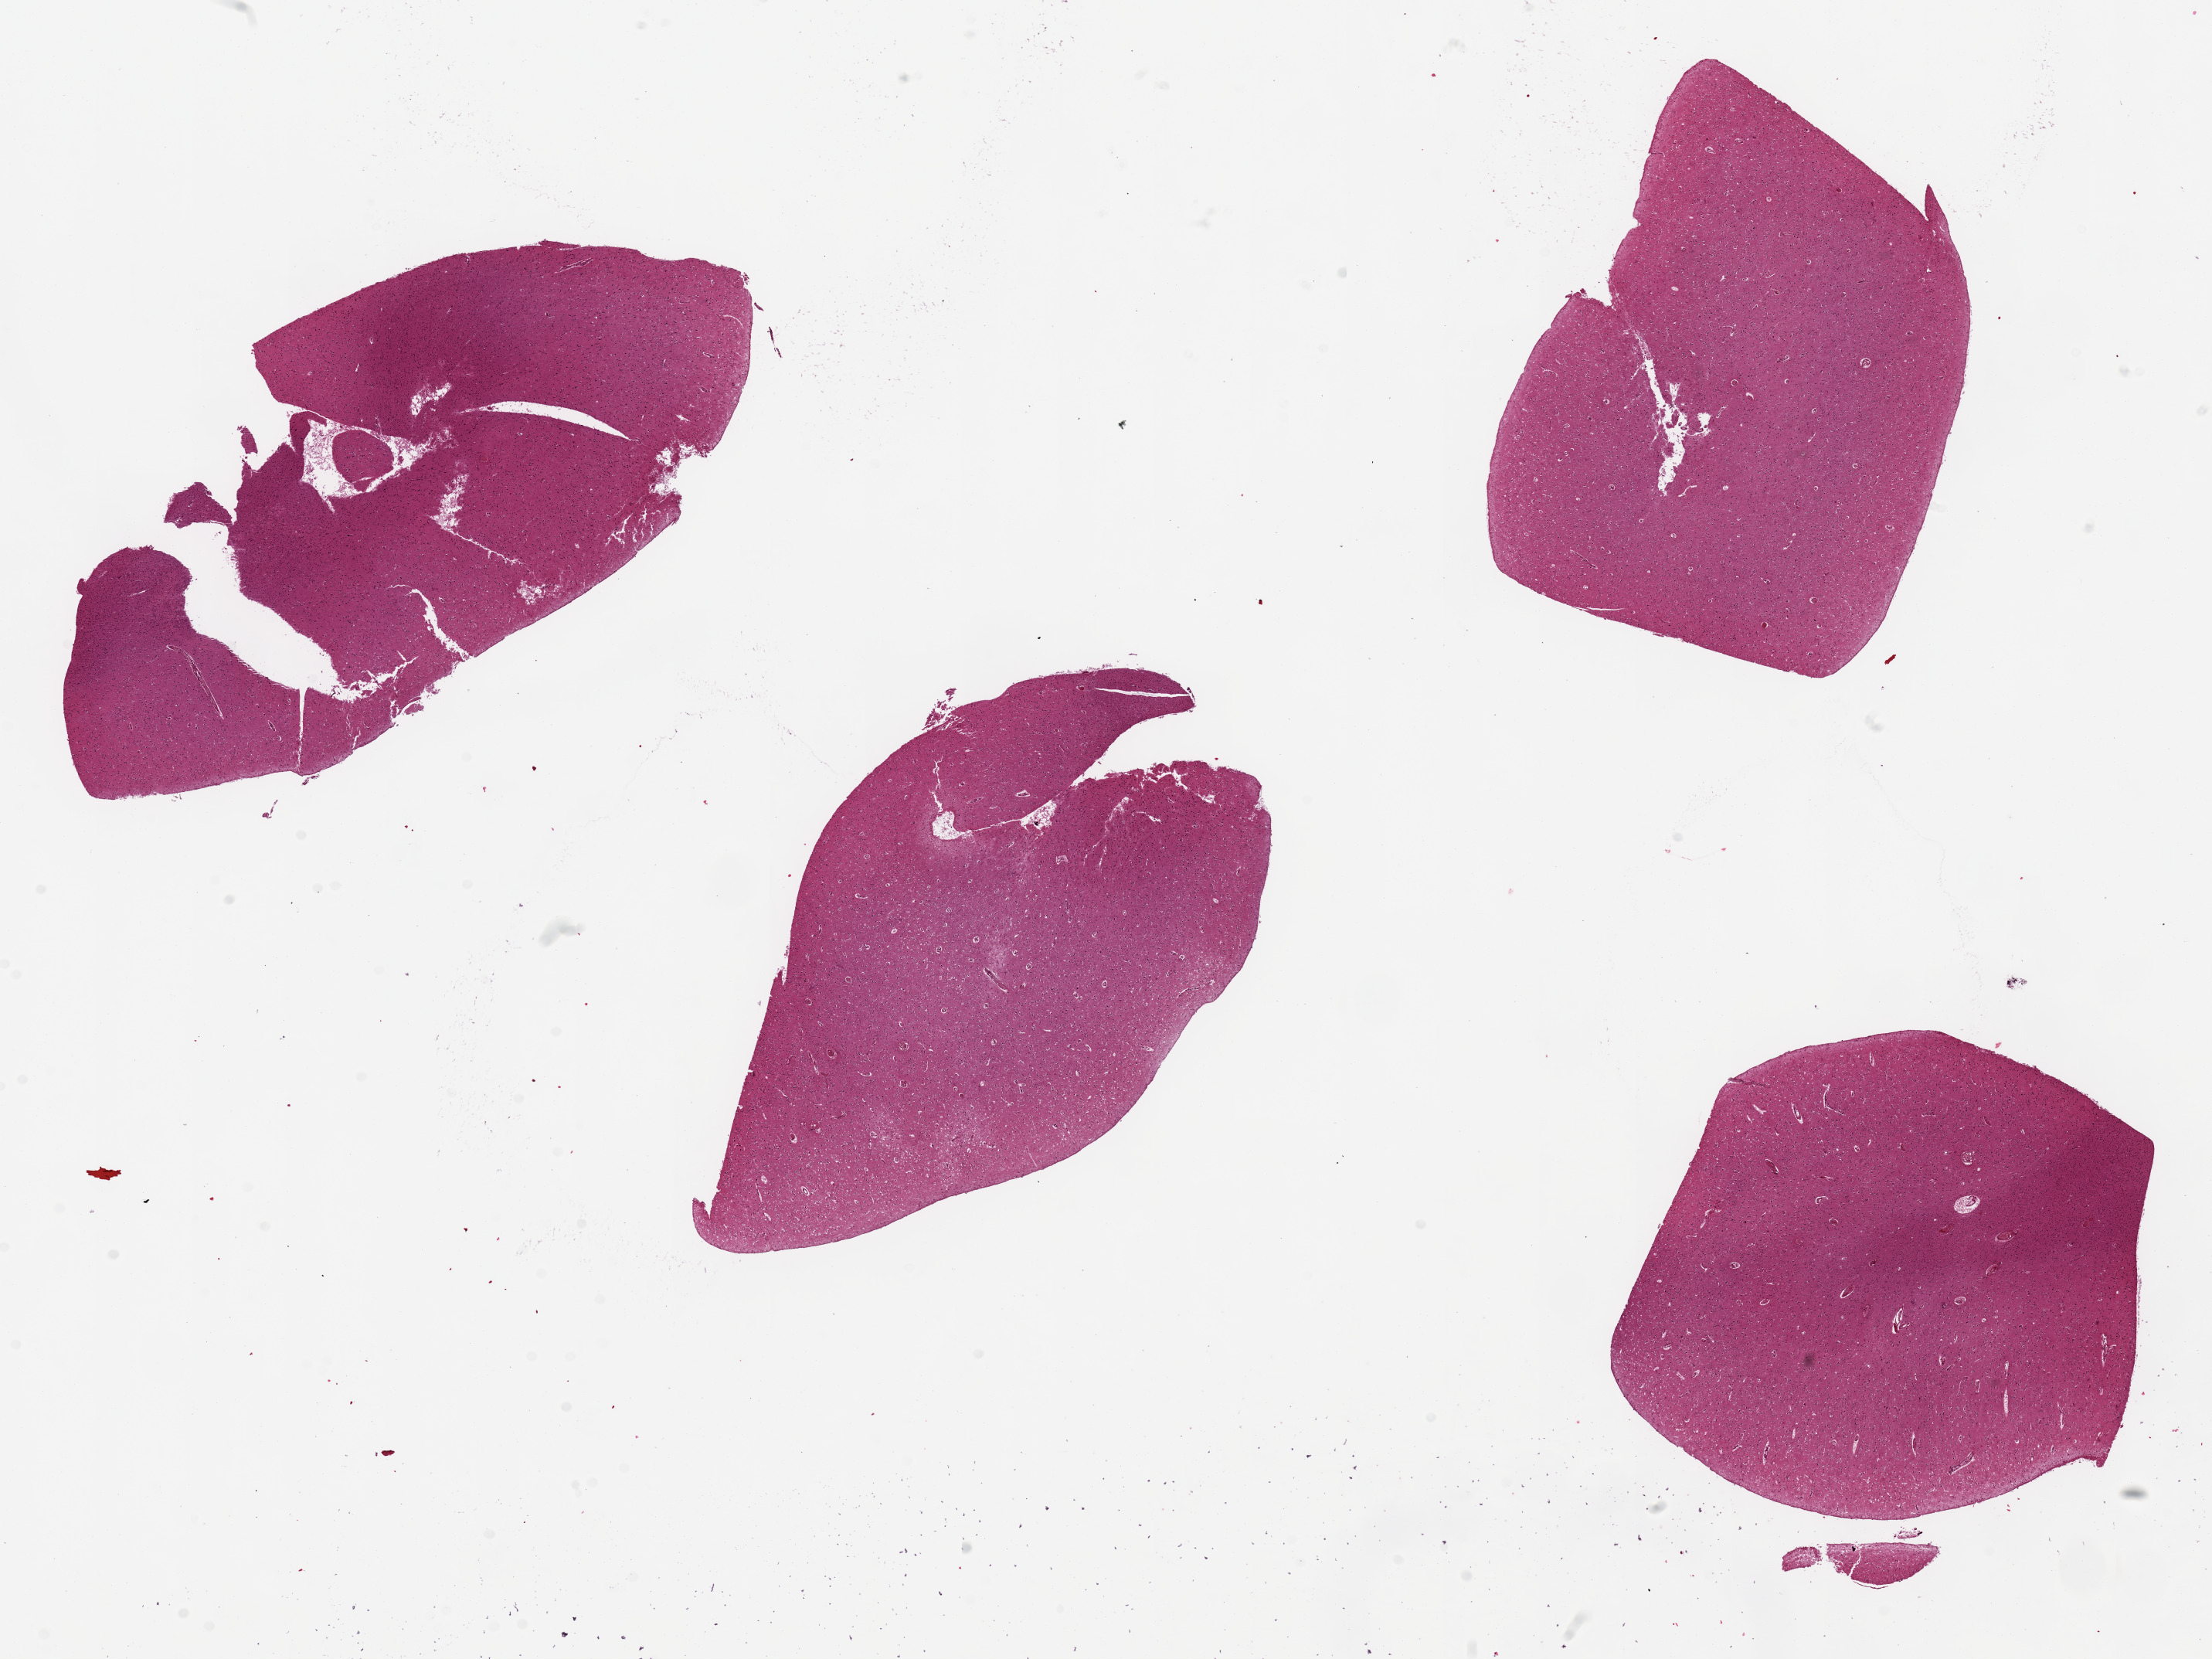
H&E whole-slide image, shown as a low-resolution overview of the whole scanned area (about 22.6 x 17.0 mm, acquisition: 20x scan). PAXgene-fixed paraffin-embedded (PFPE) section. Sampled site (target tissue): cerebral cortex. Tissue donor sample.
Pathologist's review note for this sample: 4 pieces, ~ 7x4mm.